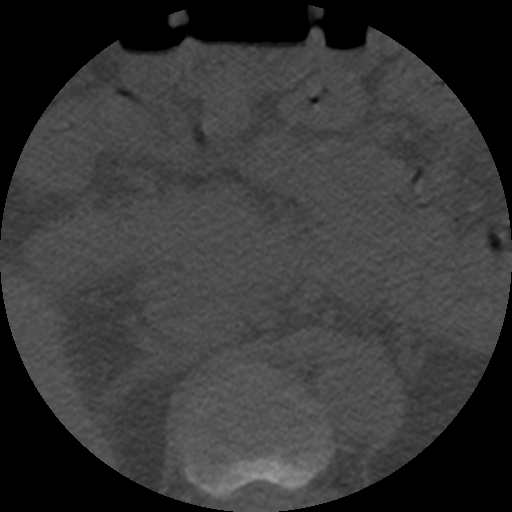
CT including the spine, one axial slice; position 230 of 508 along the scan axis; bone window (W 1800 / L 400 HU); 1.25 mm slice thickness; 512 × 512 image matrix, field of view 160 × 160 mm. Patient age 57 years. Case-level facts recorded for this patient, not image findings: primary cancer: prostate.
Outlined on this slice (semi-automatic segmentation, software-assisted and operator-edited):
- T11 vertebra: bounding box (x1, y1, x2, y2) in pixels: (185, 429, 330, 498)